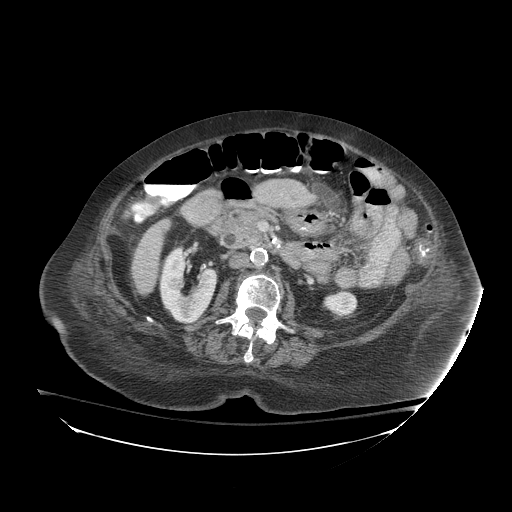
Contrast-enhanced abdominal CT (liver protocol), one axial slice. Position 24 of 81 along the scan axis. 140 kVp. Soft-tissue window (W 400 / L 40 HU). 2.5 mm slice thickness. 512 × 512 image matrix, field of view 500 × 500 mm. From the clinical record (not read from this slice): diagnosis: hepatocellular carcinoma (patient treated with transarterial chemoembolisation; whether this scan precedes or follows treatment is not stated here); TNM stage (as recorded): Stage-I; Child-Pugh class: B; tumour differentiation: well-moderately differentiated; tumour nodularity: uninodular.
Annotated regions visible in this slice (semi-automatic segmentation, software-assisted and operator-edited):
- liver parenchyma outside the tumour (the mass and vessels are separate outlines, so this box may not span the whole liver): box from (x=132, y=218) to (x=170, y=294) px